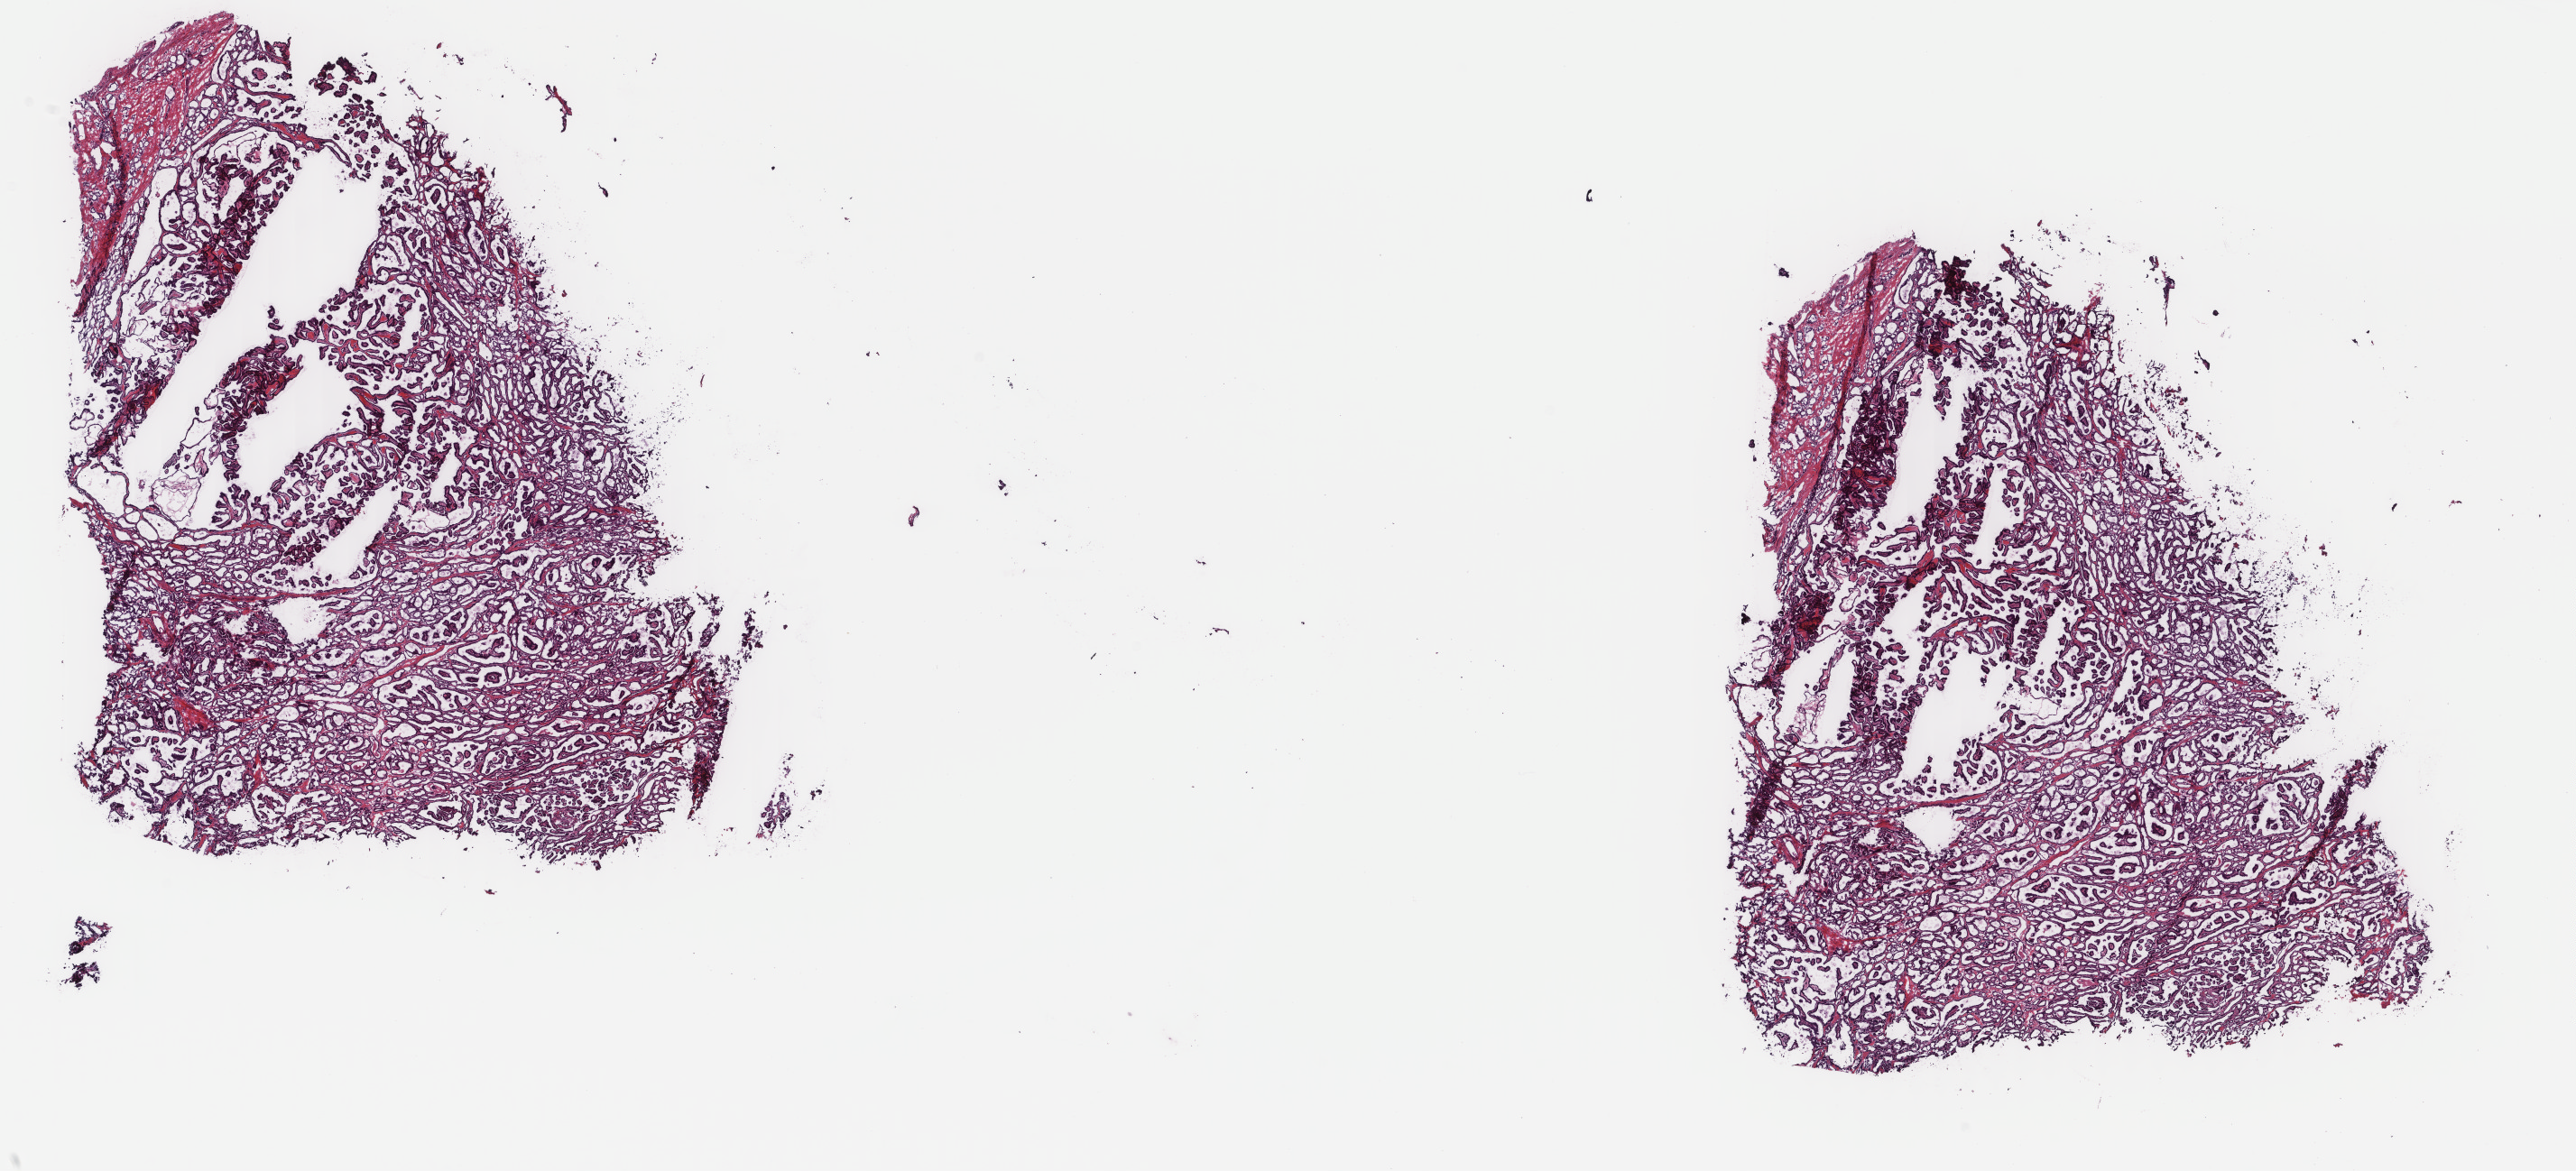
Digitized Hematoxylin and eosin (H&E) stained tissue section (whole slide) — shown as a low-resolution overview of the whole scanned area (about 22.7 x 10.3 mm, acquisition: 40x scan), frozen section, sample: primary tumour, thyroid. Female patient; age at initial diagnosis 50 years. Pathologist review of this section (percent, as recorded): tumour cells 95%, tumour nuclei 85%, normal cells 0%, stromal cells 5%, necrosis 0%. Inflammatory infiltration, as recorded: lymphocyte infiltration 2%, monocyte infiltration 0%, neutrophil infiltration 0%.
Laterality: bilateral. Histologic diagnosis: Papillary adenocarcinoma, NOS. AJCC pathologic stage: III.